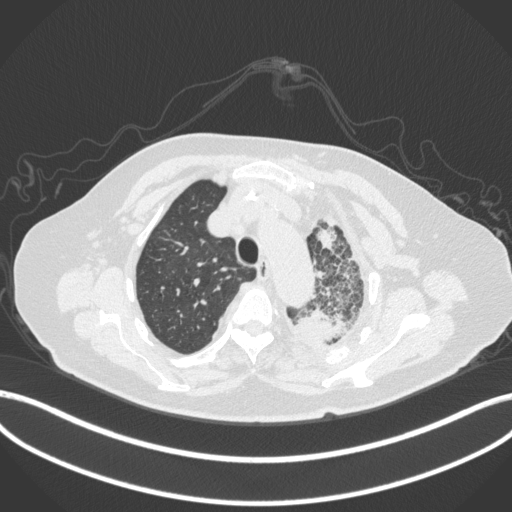
Chest CT, one axial slice; slice 311 of 399 in the series (ordered by position); reconstruction kernel B31f; 120 kVp; lung window (W 1500 / L -600 HU); 1 mm slice thickness; 512 × 512 image matrix, field of view 400 × 400 mm. Patient: female, 75 years. Case-level facts recorded for this patient, not image findings: clinical TNM (as recorded): T3 N3 M1.
Structures marked on this image (rectangle marked by the reading radiologist):
- lung tumour (recorded histology: adenocarcinoma): box from (x=291, y=308) to (x=348, y=348) px